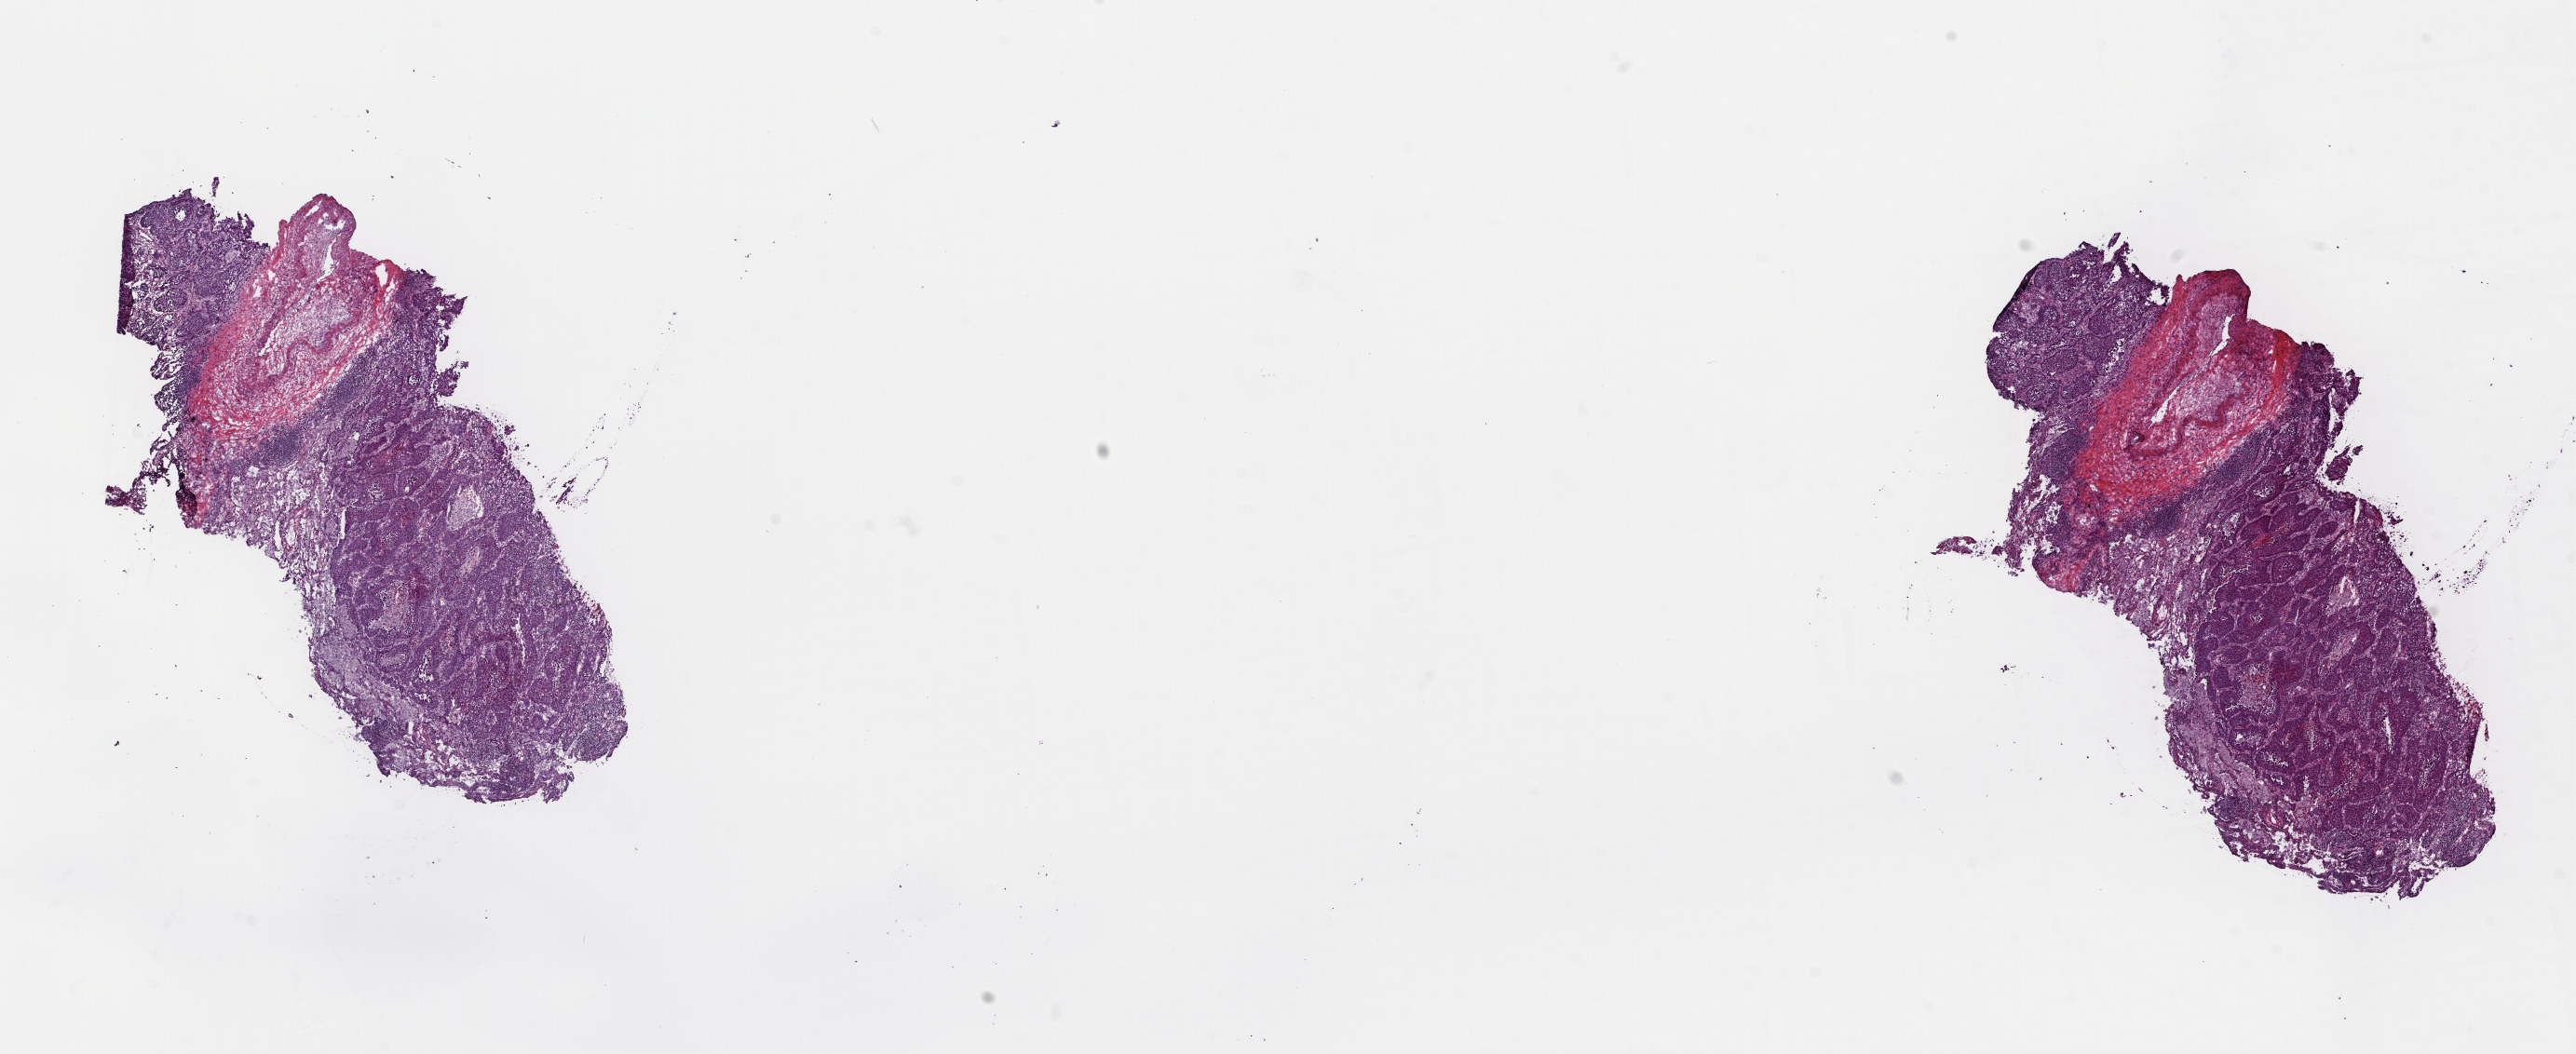
Digitized H&E-stained tissue section (whole slide), whole scanned area (about 21.7 x 8.9 mm) shown as a low-resolution overview, frozen section, lung, primary tumour sample. Male patient; age at initial diagnosis 56 years. Slide review estimates, as recorded: tumour cells 42%, tumour nuclei 70%, normal cells 0%, stromal cells 50%, necrosis 8%. Inflammatory infiltration, as recorded: lymphocyte infiltration 15%, monocyte infiltration 3%, neutrophil infiltration 2%.
Pathologic diagnosis: Squamous cell carcinoma, NOS (lower lobe, lung). AJCC pathologic stage: IIB (6th edition). Laterality: right.